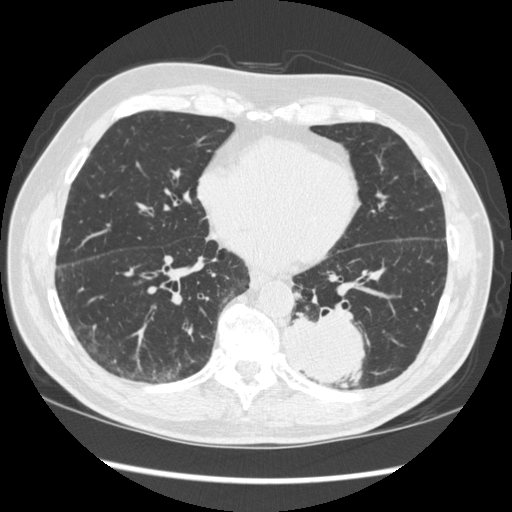
Low-dose screening chest CT, axial slice; baseline screening round; lung window (W 1500 / L -600 HU); 1.25 mm slice thickness; standard (soft-tissue) reconstruction kernel (STANDARD); slice 126 of 348 in the series. Male participant, aged 72 years at enrolment.
Expert reader's lesion annotation, box from (x=272, y=297) to (x=376, y=386) px. The screening reader recorded 2 non-calcified nodules or masses ≥4 mm on this exam; which of them this box marks is not recorded. Lung cancer was diagnosed 37 days after this screen: squamous cell carcinoma, NOS, left lower lobe, stage IIIA (AJCC 6th edition), 60 mm at pathology.